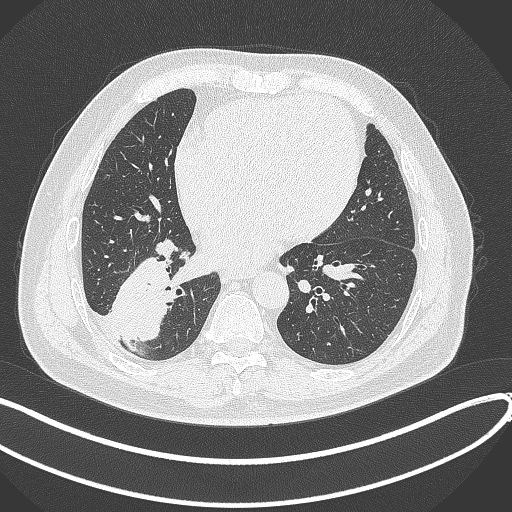
Chest CT, one axial slice. Lung window (W 1500 / L -600 HU). 512 × 512 image matrix, field of view 400 × 400 mm. Male patient, age 59 years.
Annotated regions visible in this slice (rectangle marked by the reading radiologist):
- lung tumour (recorded histology: adenocarcinoma): bounding box (x1, y1, x2, y2) in pixels: (108, 255, 174, 347)